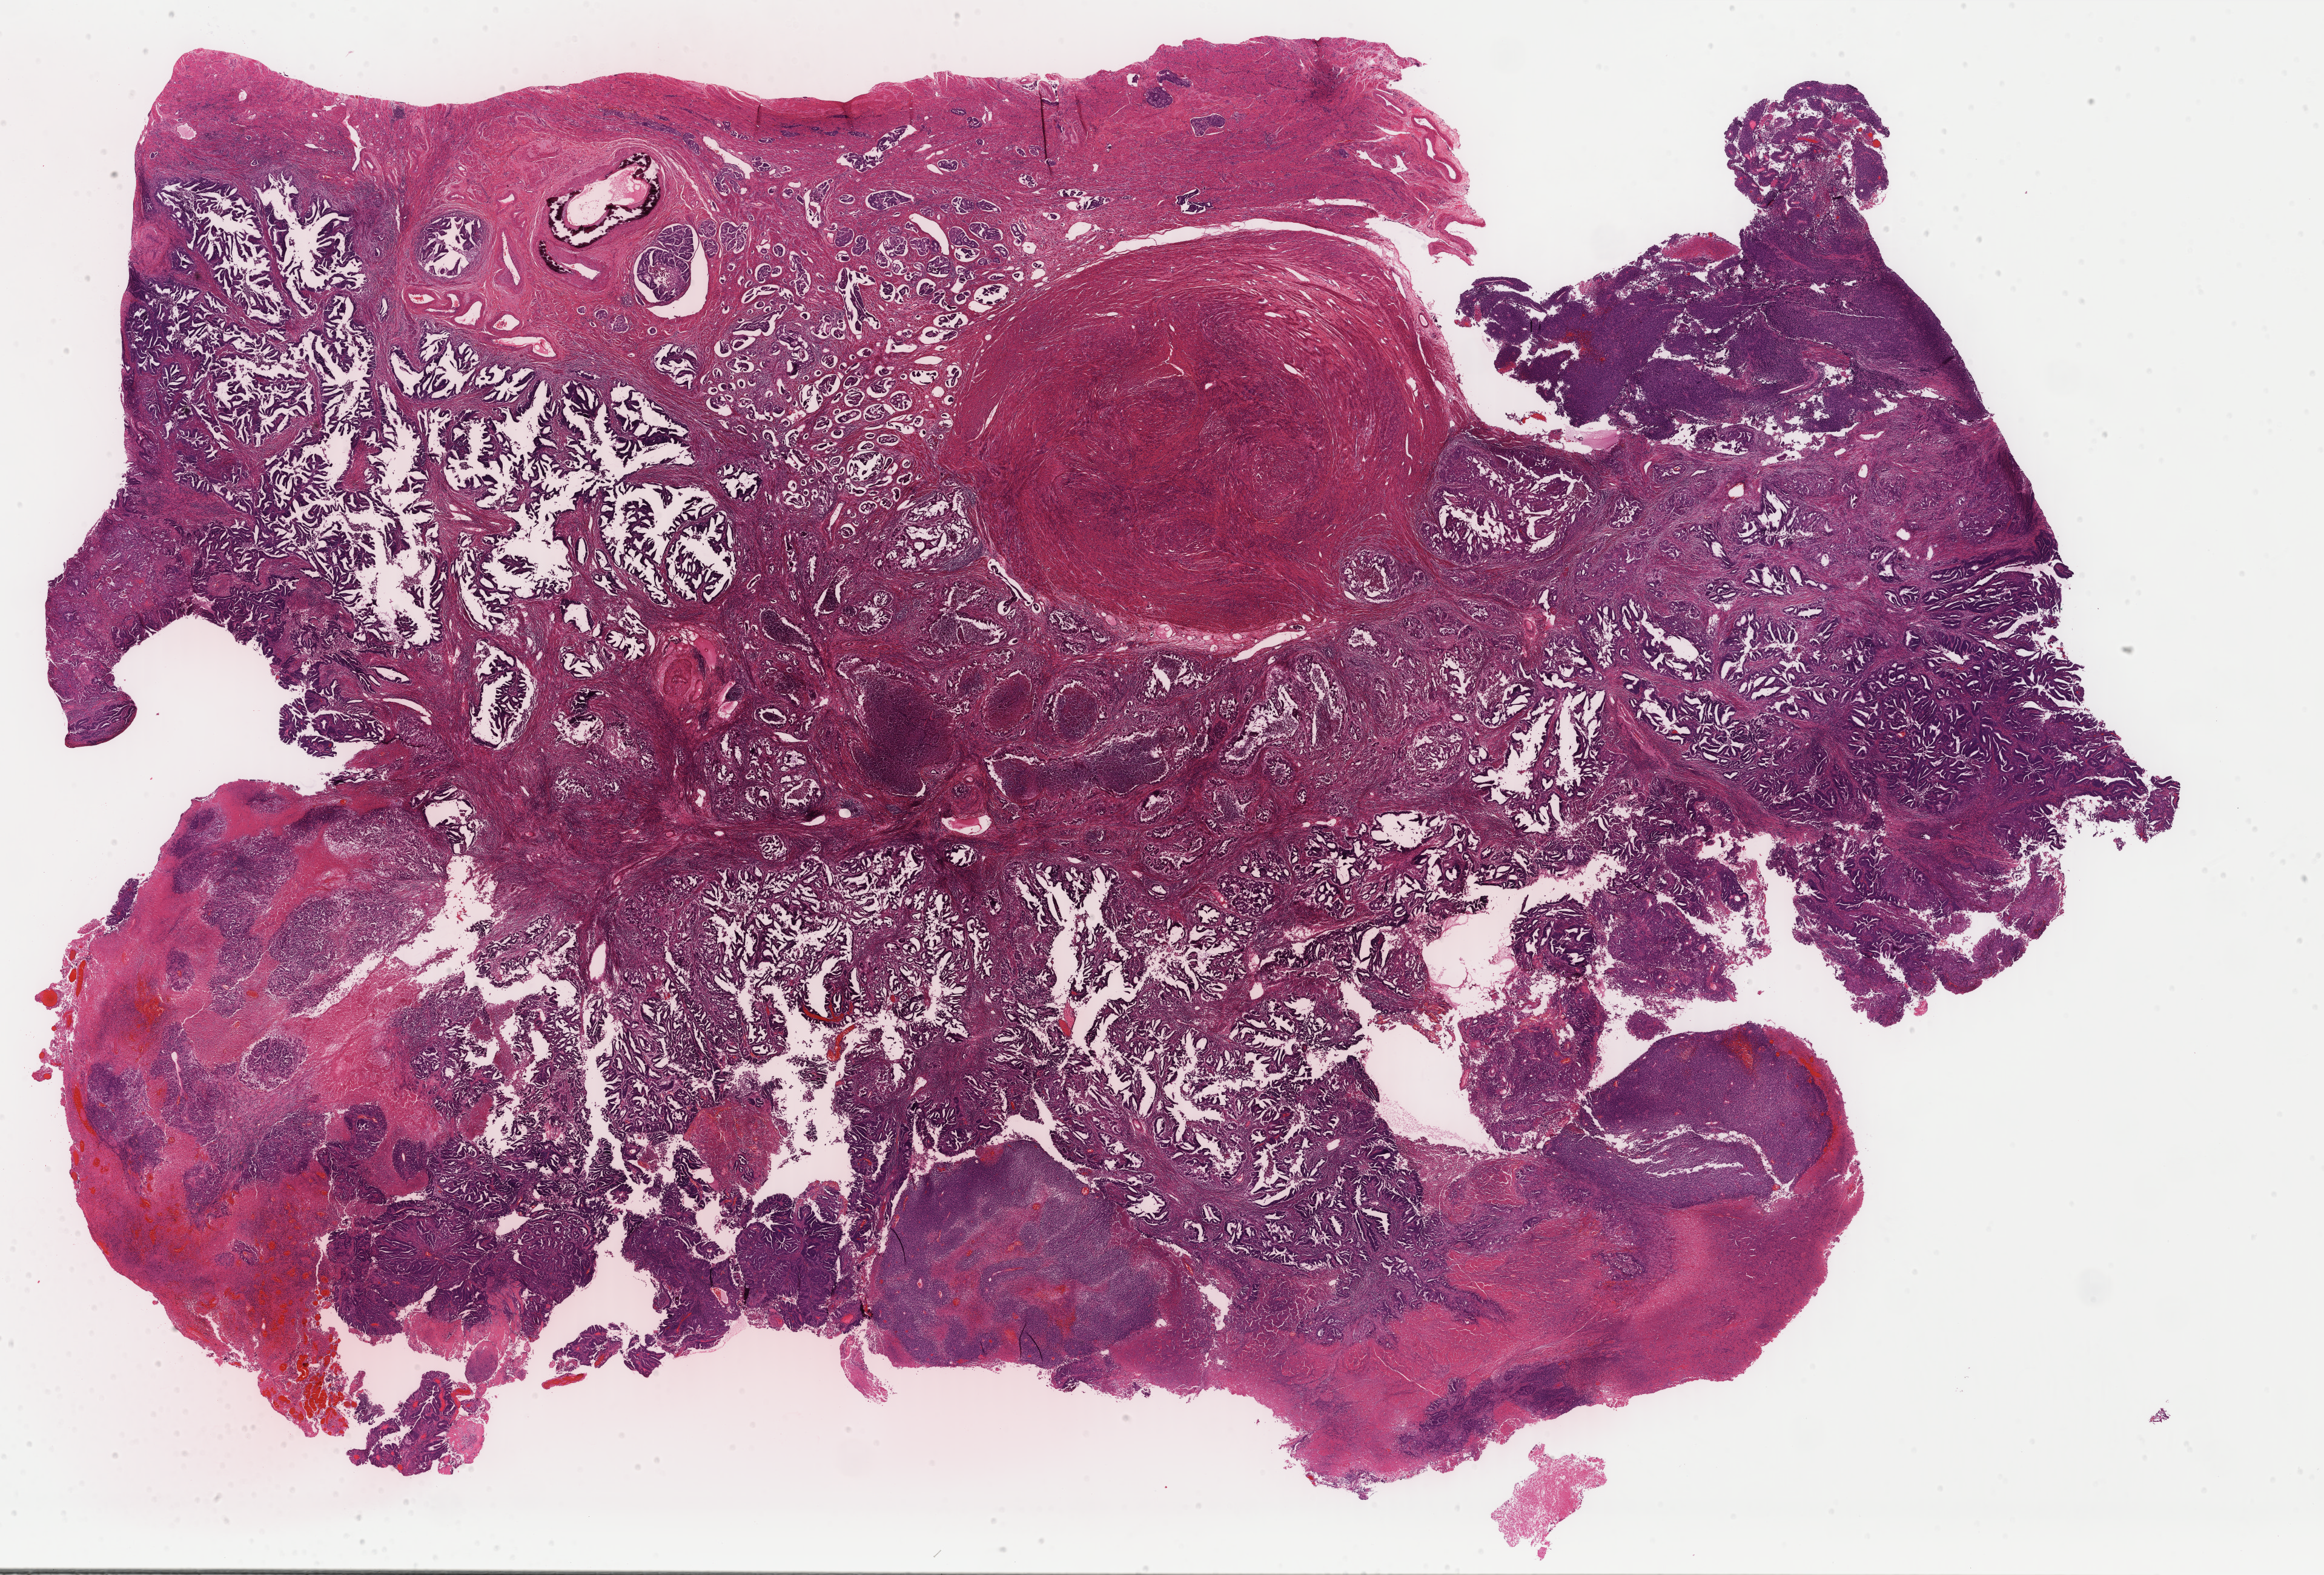
Whole-slide histology image, Hematoxylin and eosin (H&E) stained — shown as a low-resolution overview of the whole scanned area (about 30.5 x 20.6 mm, from a 40x scan); formalin-fixed paraffin-embedded (FFPE) diagnostic section; primary tumour sample from the uterus. Patient: female, age at initial diagnosis 83 years.
FIGO stage: IB. Histologic diagnosis: Mullerian mixed tumor (fundus uteri).